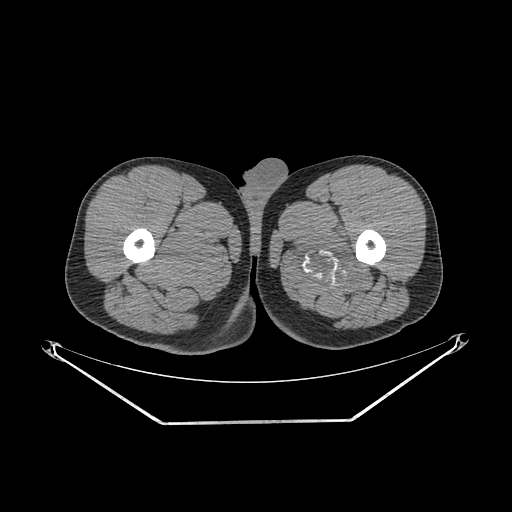
CT of an extremity soft-tissue mass (from a PET/CT study), one axial slice. Position 255 of 267 along the scan axis. Reconstruction kernel SOFT. 140 kVp. Soft-tissue window (W 400 / L 40 HU). 3.75 mm slice thickness. 512 × 512 image matrix, field of view 500 × 500 mm. Male patient. Case-level facts recorded for this patient, not image findings: histological type: extraskeletal osteosarcoma; grade: high; site of the primary tumour: left adductur.
Structures marked on this image (expert contour drawn on MRI and transferred to this co-registered scan by the dataset authors):
- gross tumour volume (mass): bounding box <288,217,378,295> (left, top, right, bottom; pixels)